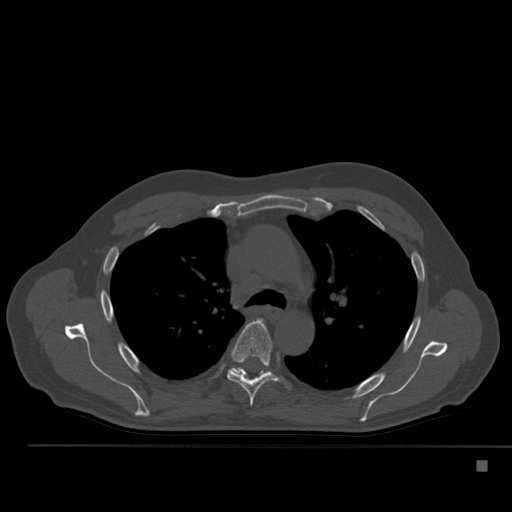
CT including the spine, one axial slice; position 364 of 517 along the scan axis; reconstruction kernel Br40s; bone window (W 1800 / L 400 HU); 1.5 mm slice thickness; 512 × 512 image matrix, field of view 408 × 408 mm. Patient: male, 70 years. Case-level facts recorded for this patient, not image findings: primary cancer: renal.
Annotated regions visible in this slice (semi-automatically segmented with operator editing):
- T5 vertebra: bounding box [x1, y1, x2, y2] px = [227, 320, 291, 406]
- T6 vertebra: [232, 367, 262, 376]